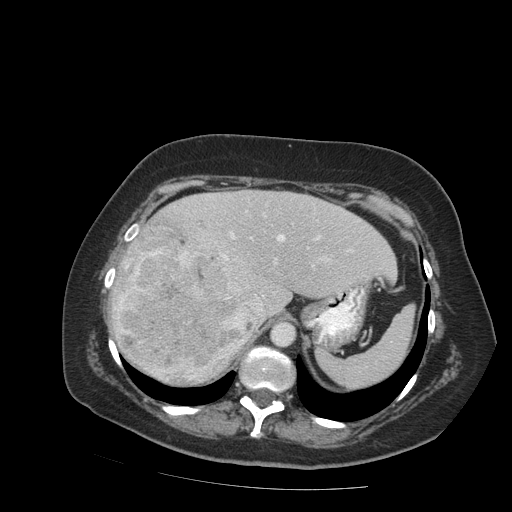
Contrast-enhanced abdominal CT (liver protocol), one axial slice. Position 63 of 99 along the scan axis. Reconstruction kernel STANDARD. 140 kVp. Soft-tissue window (W 400 / L 40 HU). 512 × 512 image matrix, field of view 400 × 400 mm. From the clinical record (not read from this slice): diagnosis: hepatocellular carcinoma (patient treated with transarterial chemoembolisation; whether this scan precedes or follows treatment is not stated here); TNM stage (as recorded): Stage-IVB; Child-Pugh class: A; tumour differentiation: moderately differentiated; tumour nodularity: uninodular.
Outlined on this slice (semi-automatically segmented with operator editing):
- abdominal aorta: bounding box <272,322,295,346> (left, top, right, bottom; pixels)
- liver parenchyma outside the tumour (the mass and vessels are separate outlines, so this box may not span the whole liver): <112,190,396,384>
- mass: <114,224,256,385>
- liver vessels: <131,211,353,310>